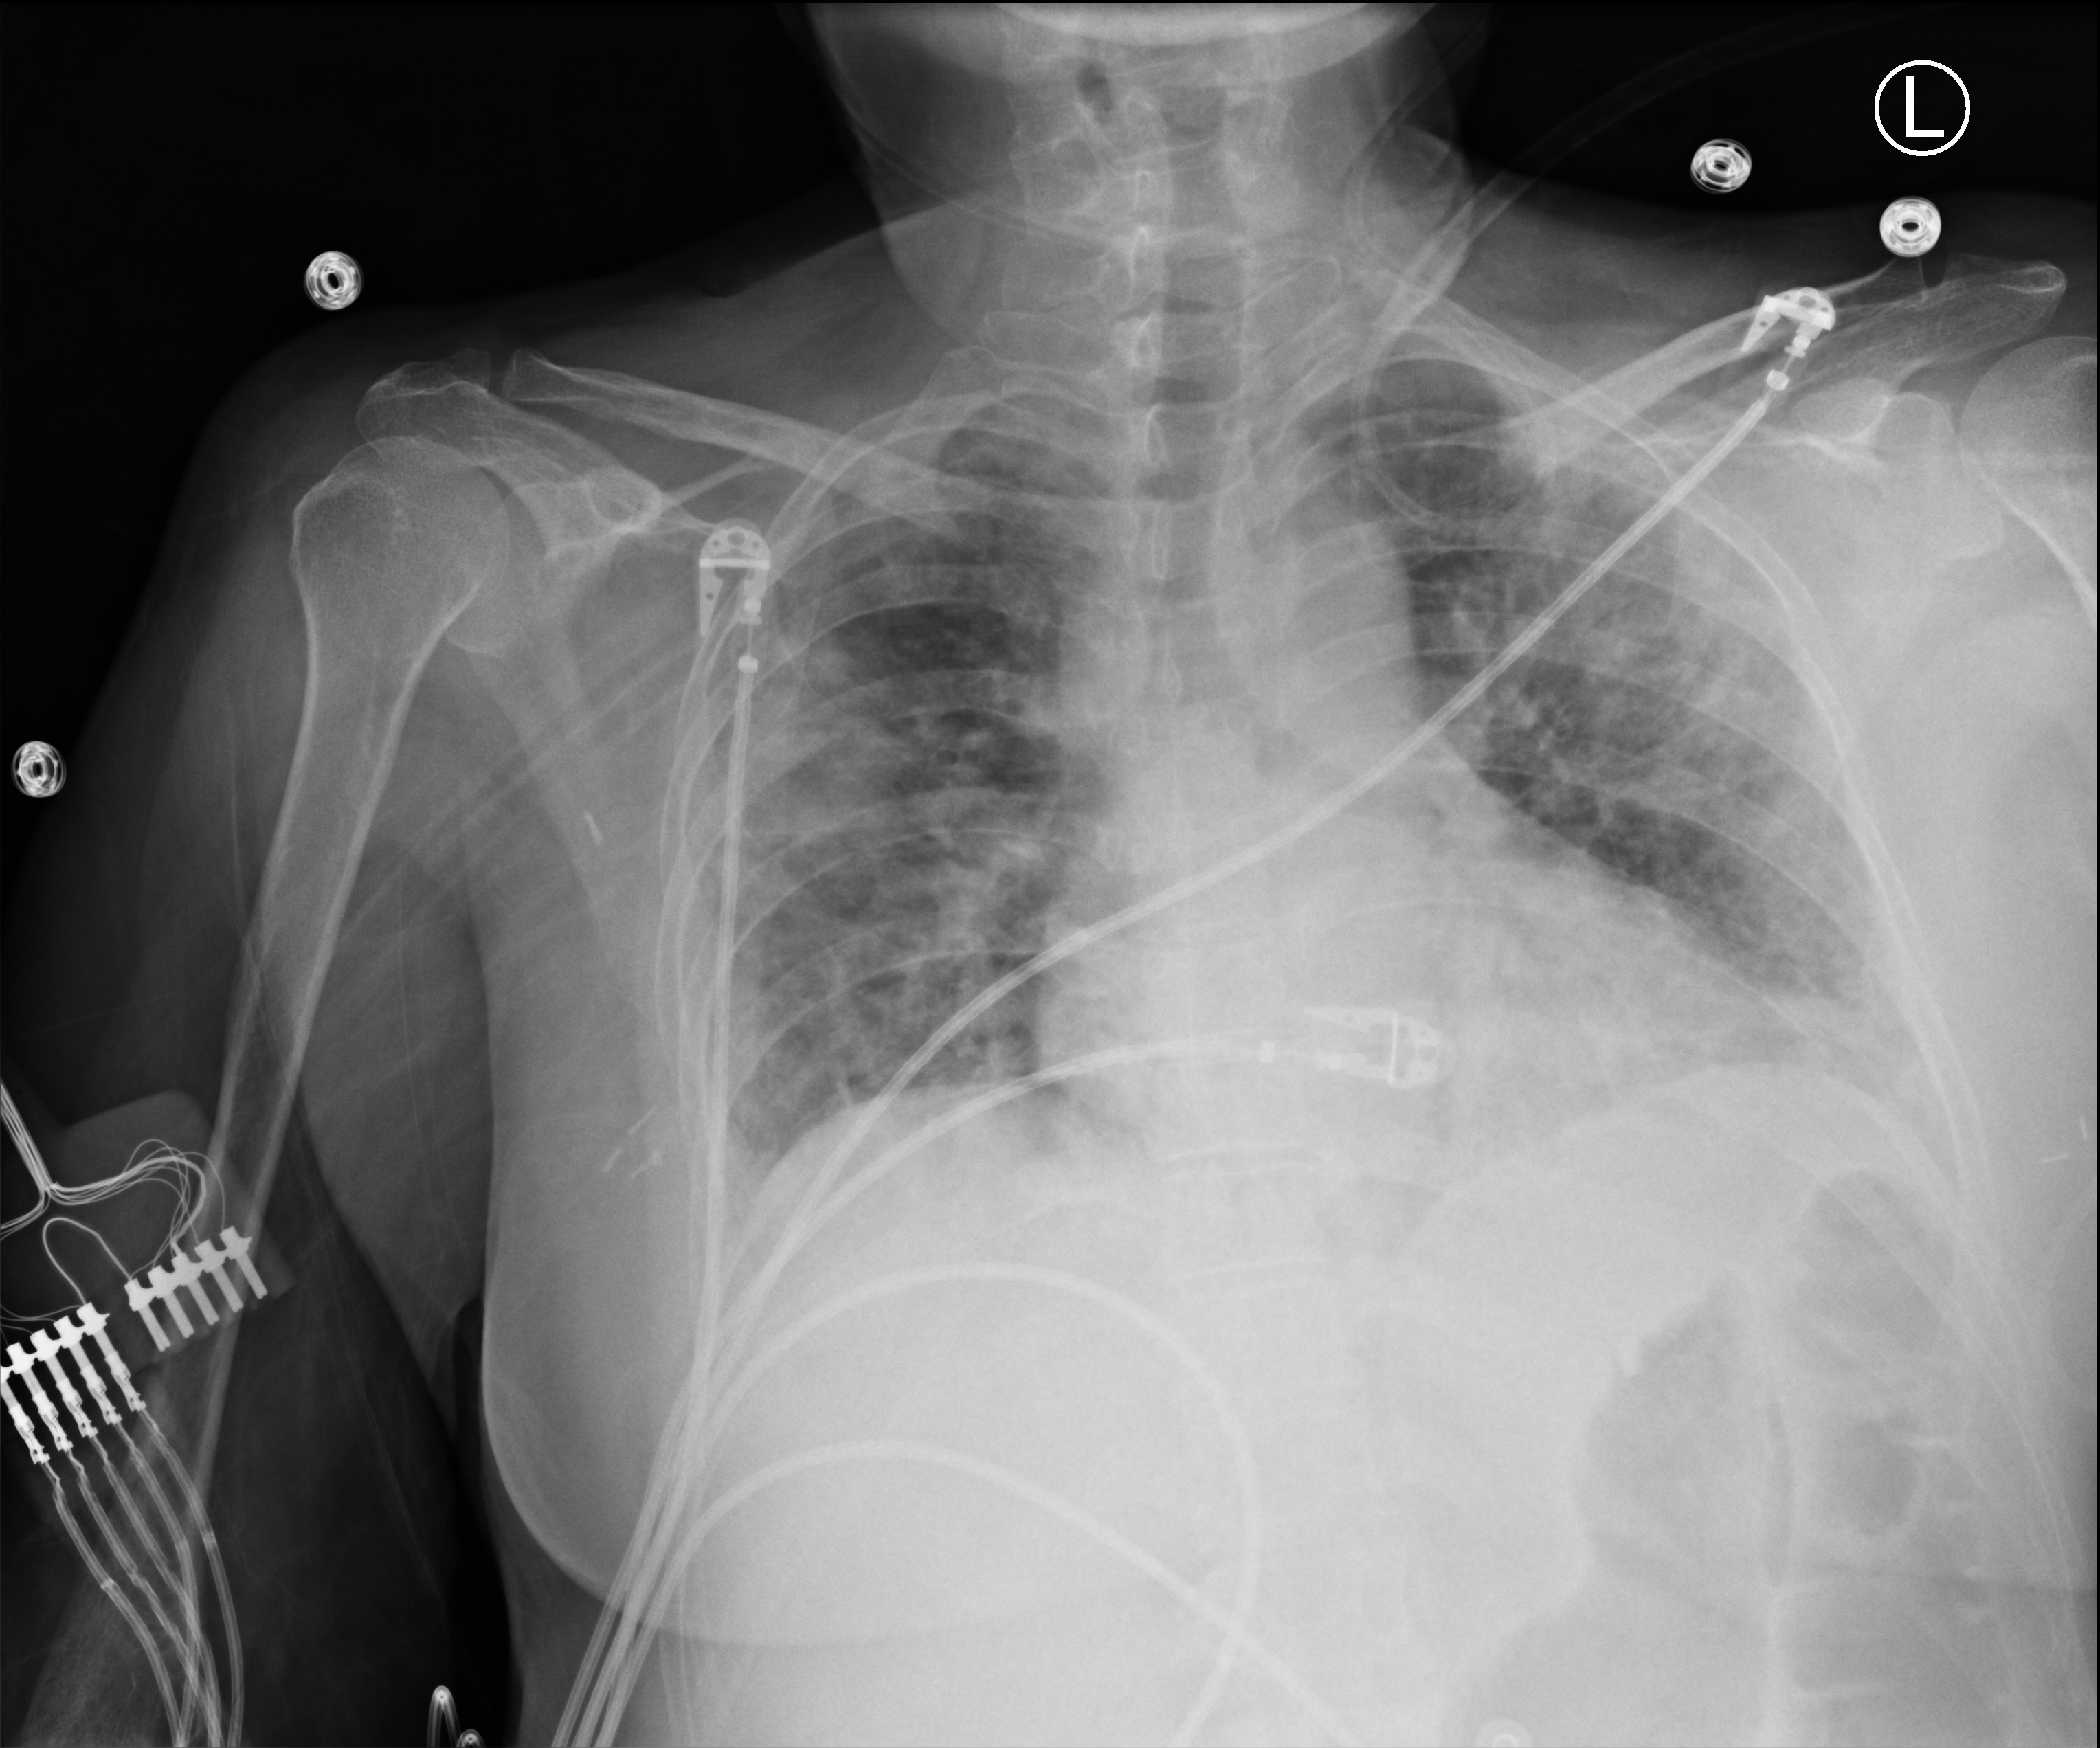
Portable chest radiograph; anteroposterior (AP) projection. Female patient hospitalised with COVID-19, age 18–59 years.
From the hospital-stay record, not from the radiograph (when in the stay this image was taken is not recorded):
- smoking status (admission record): never